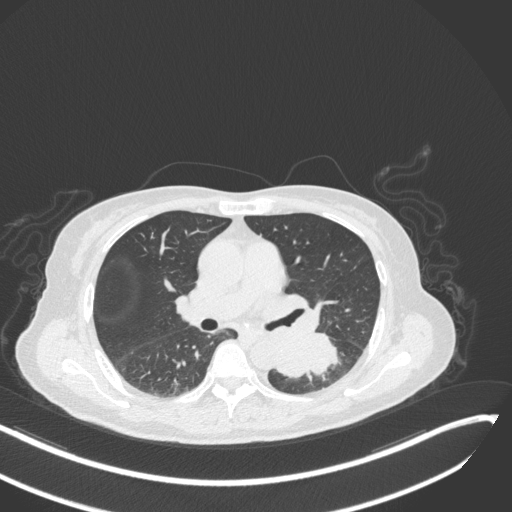
Chest CT, one axial slice; slice 158 of 342 in the series (ordered by position); reconstruction kernel B31f; 120 kVp; lung window (W 1500 / L -600 HU); 512 × 512 image matrix, field of view 400 × 400 mm. Patient: female, 64 years. Case-level facts recorded for this patient, not image findings: clinical TNM (as recorded): T3 N1 M1; histopathological grade: G3.
Outlined on this slice (rectangle marked by the reading radiologist):
- lung tumour (recorded histology: small cell carcinoma): box from (x=273, y=328) to (x=339, y=378) px